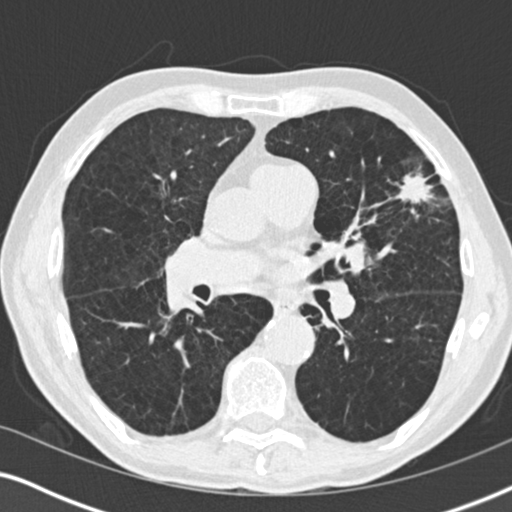
Low-dose screening chest CT, one axial slice; position 103 of 196 along the scan axis; reconstruction kernel B30f; 120 kVp; lung window (W 1500 / L -600 HU); 2 mm slice thickness; 512 × 512 image matrix, field of view 330 × 330 mm.
Annotated regions visible in this slice (outlined manually by an expert reader):
- lesion 1 (tumor, upper lobe of left lung): bounding box [x1, y1, x2, y2] px = [397, 173, 434, 205]